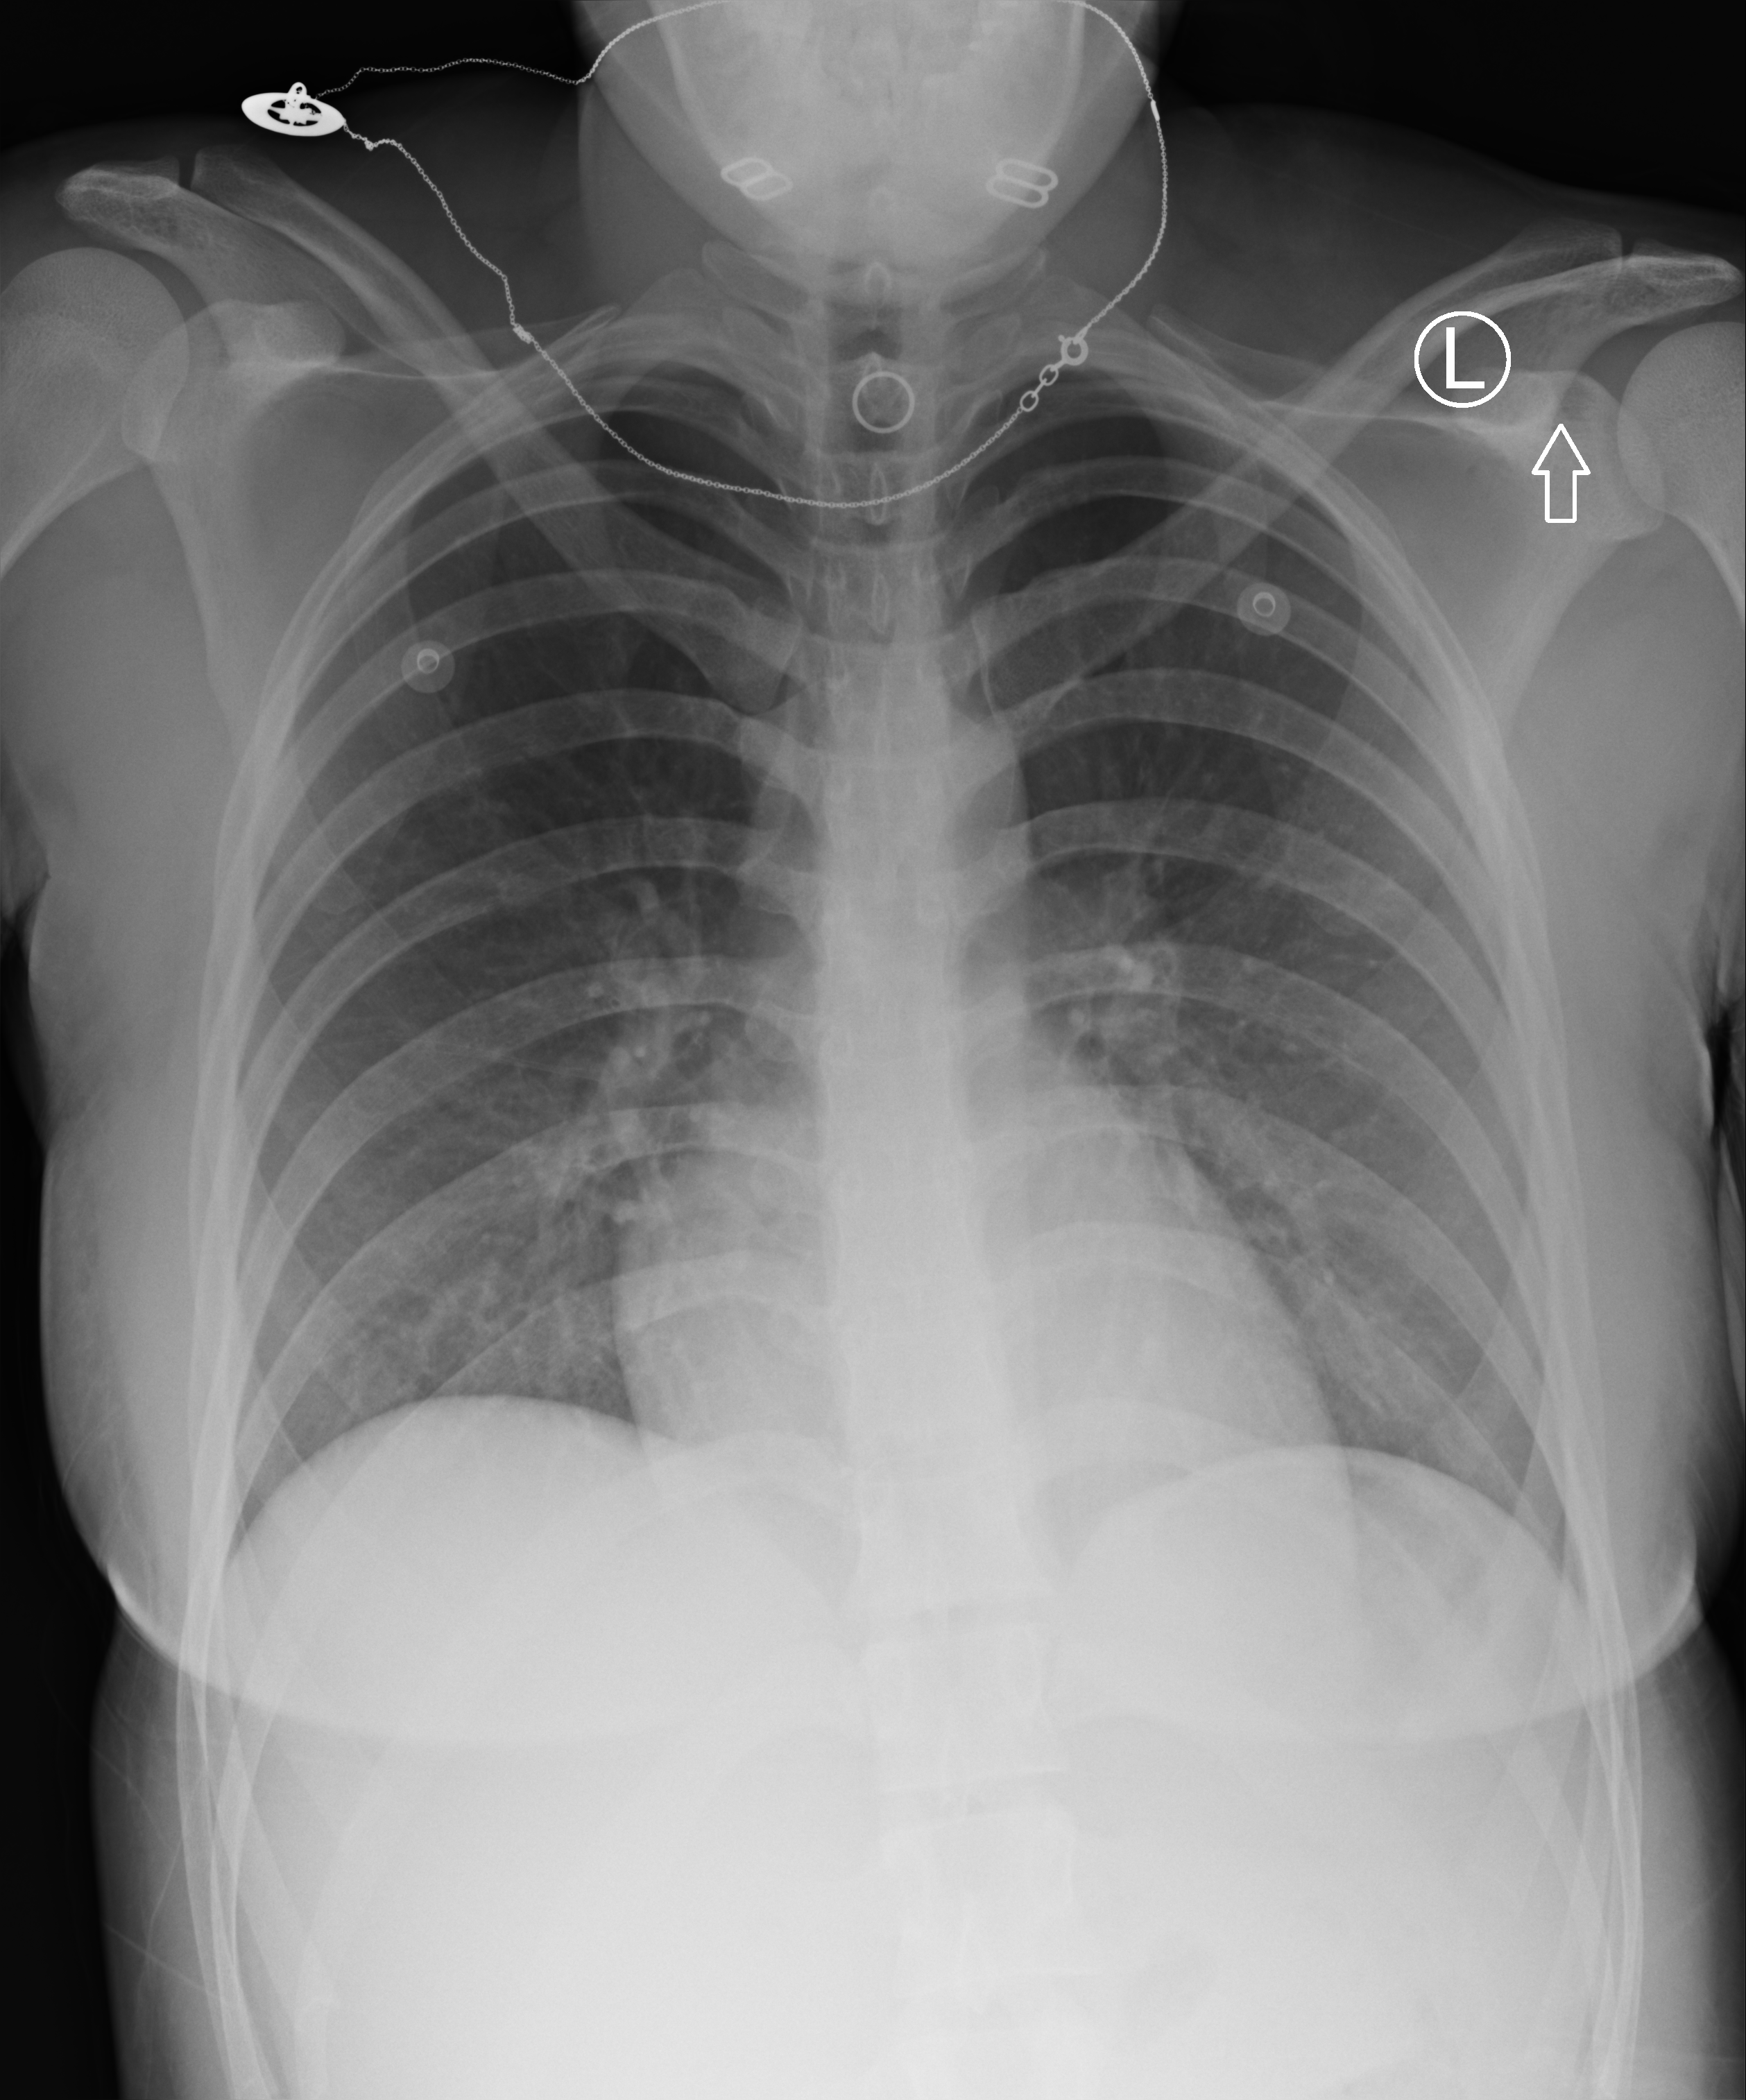
Portable chest radiograph, anteroposterior (AP) projection. Patient hospitalised with COVID-19; female, aged 18–59 years.
Admission-level facts for this patient (not findings on this image; timing relative to this image not recorded): mechanically ventilated during this hospital stay: no; length of hospital stay: 2 days; admitted to intensive care during this hospital stay: no.